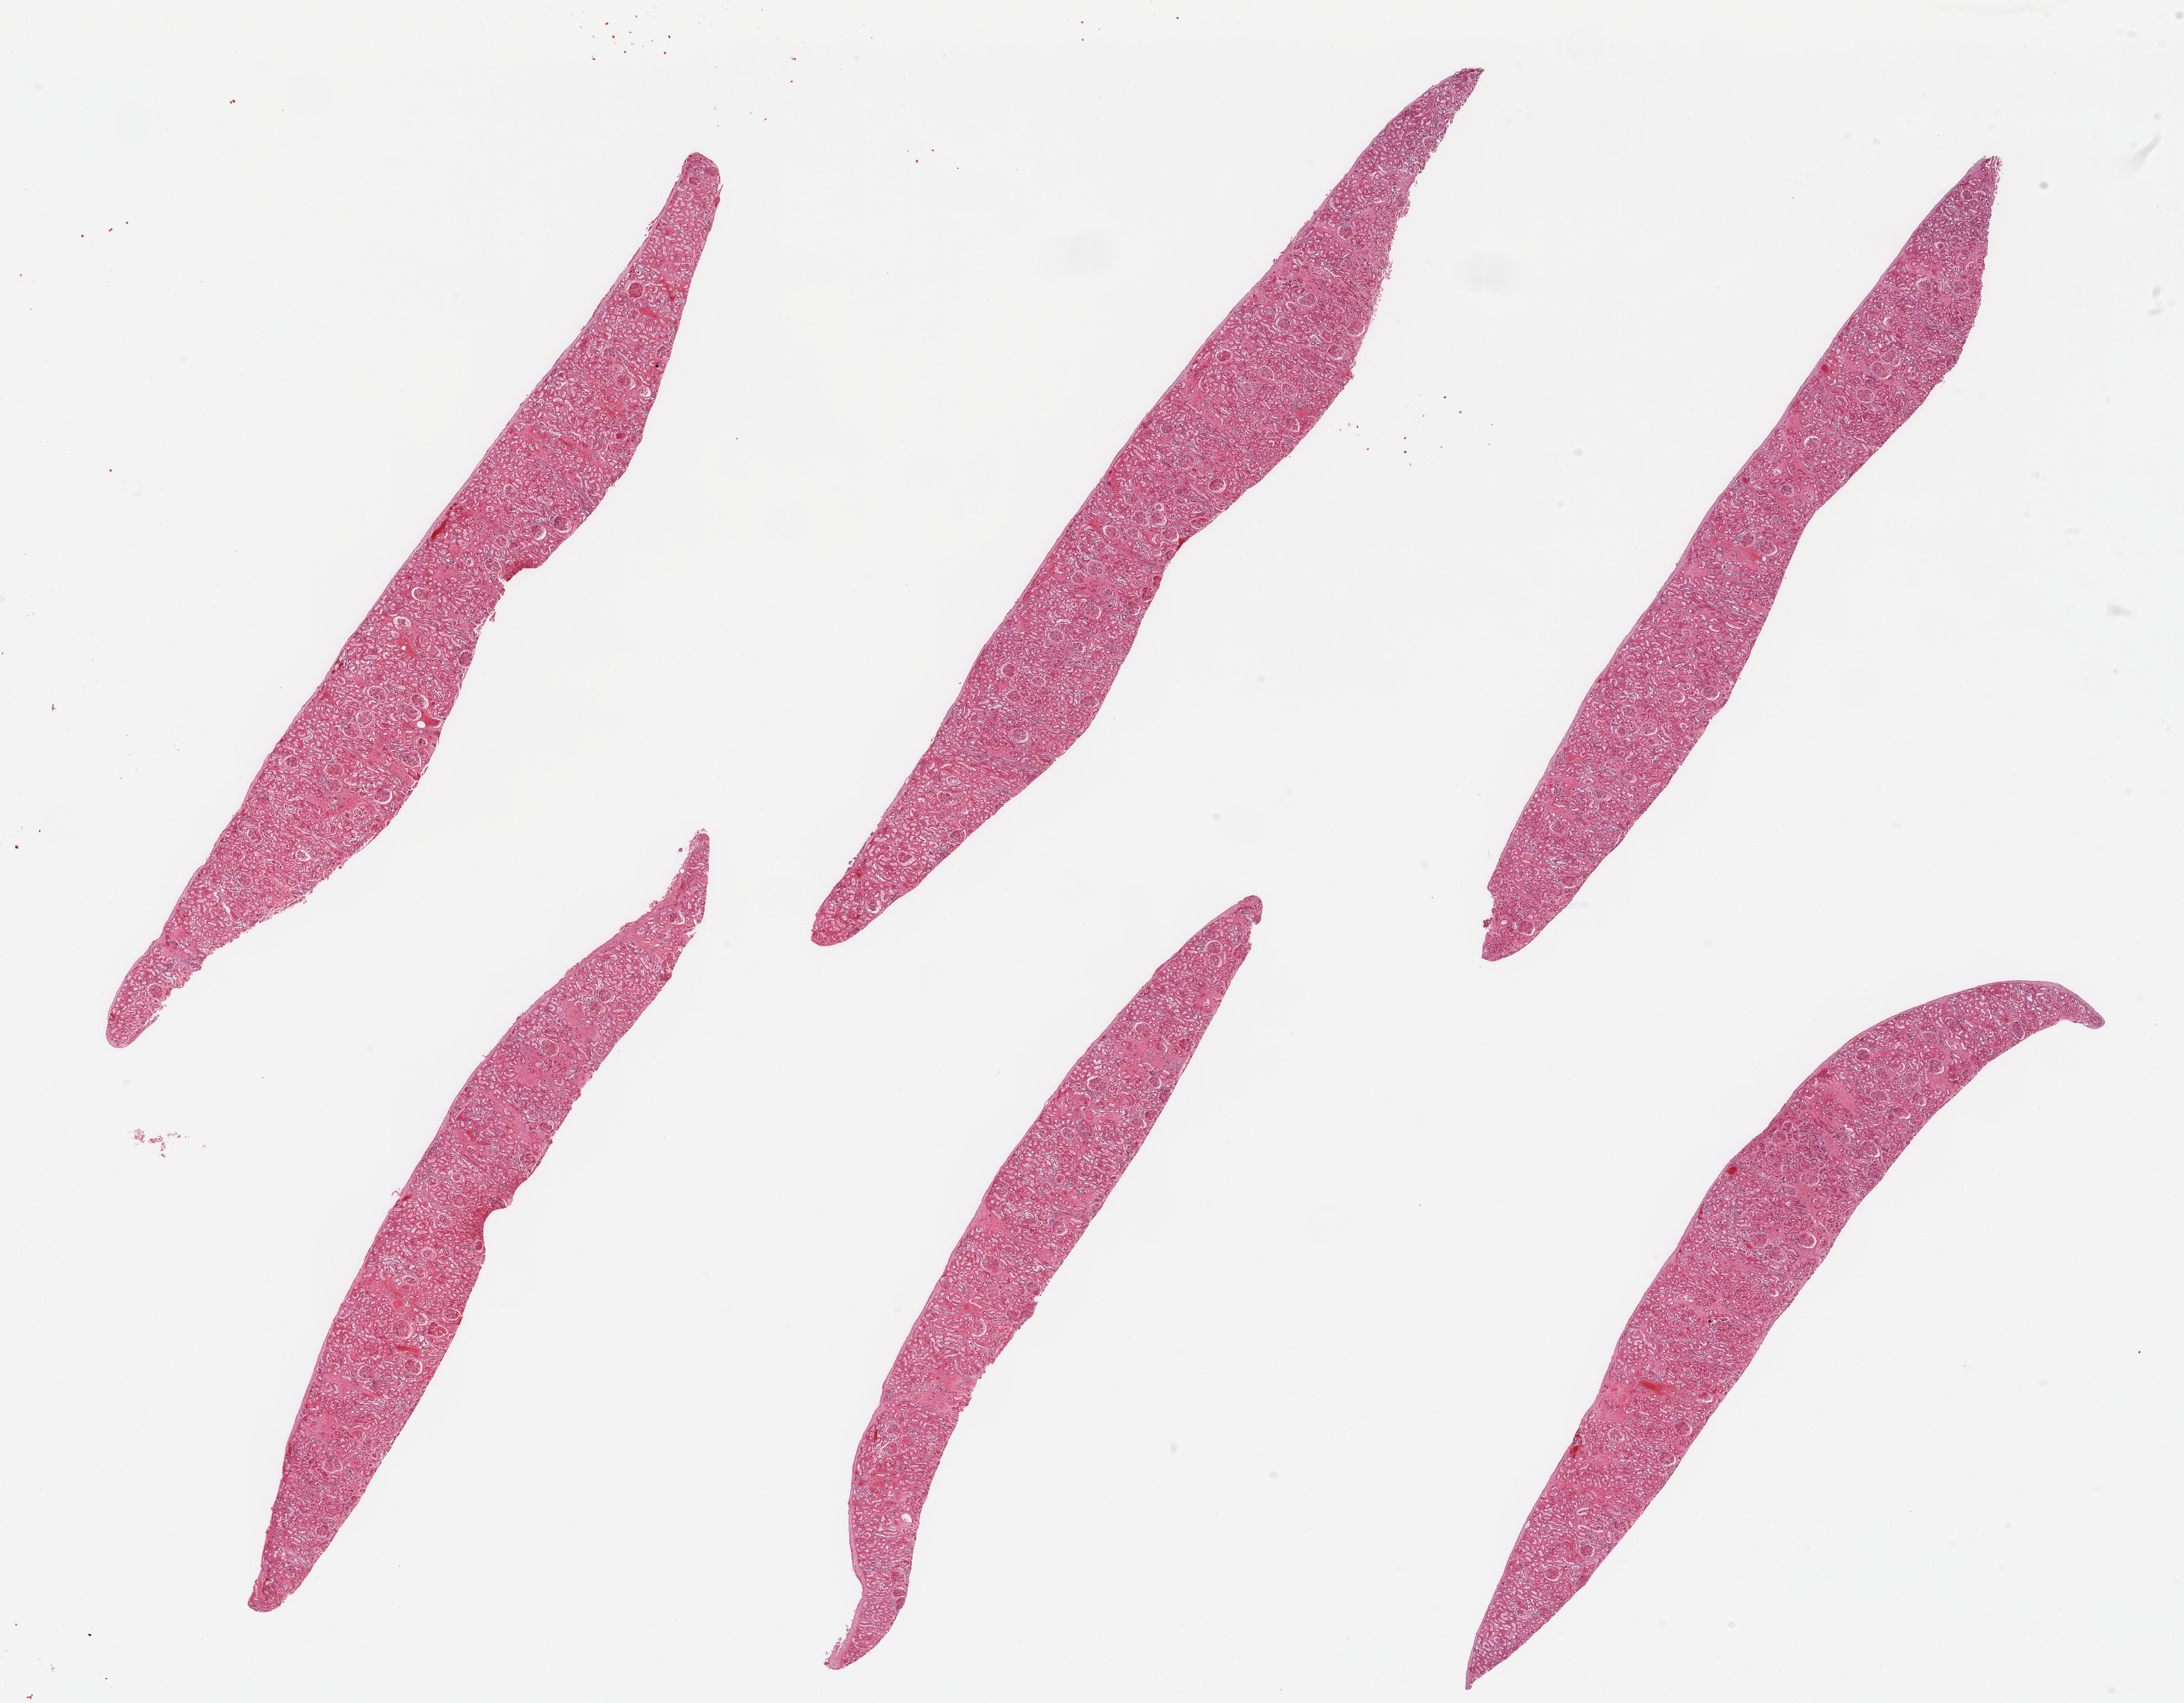
Digitized haematoxylin and eosin-stained section, whole scanned area (about 27.6 x 21.5 mm) shown as a low-resolution overview, PAXgene-fixed paraffin-embedded (PFPE) section, sampled site (target tissue): renal cortex, tissue donor sample. Male donor.
Review note (as recorded): 6 pieces; glomeruli in all sections, some sclerotic.